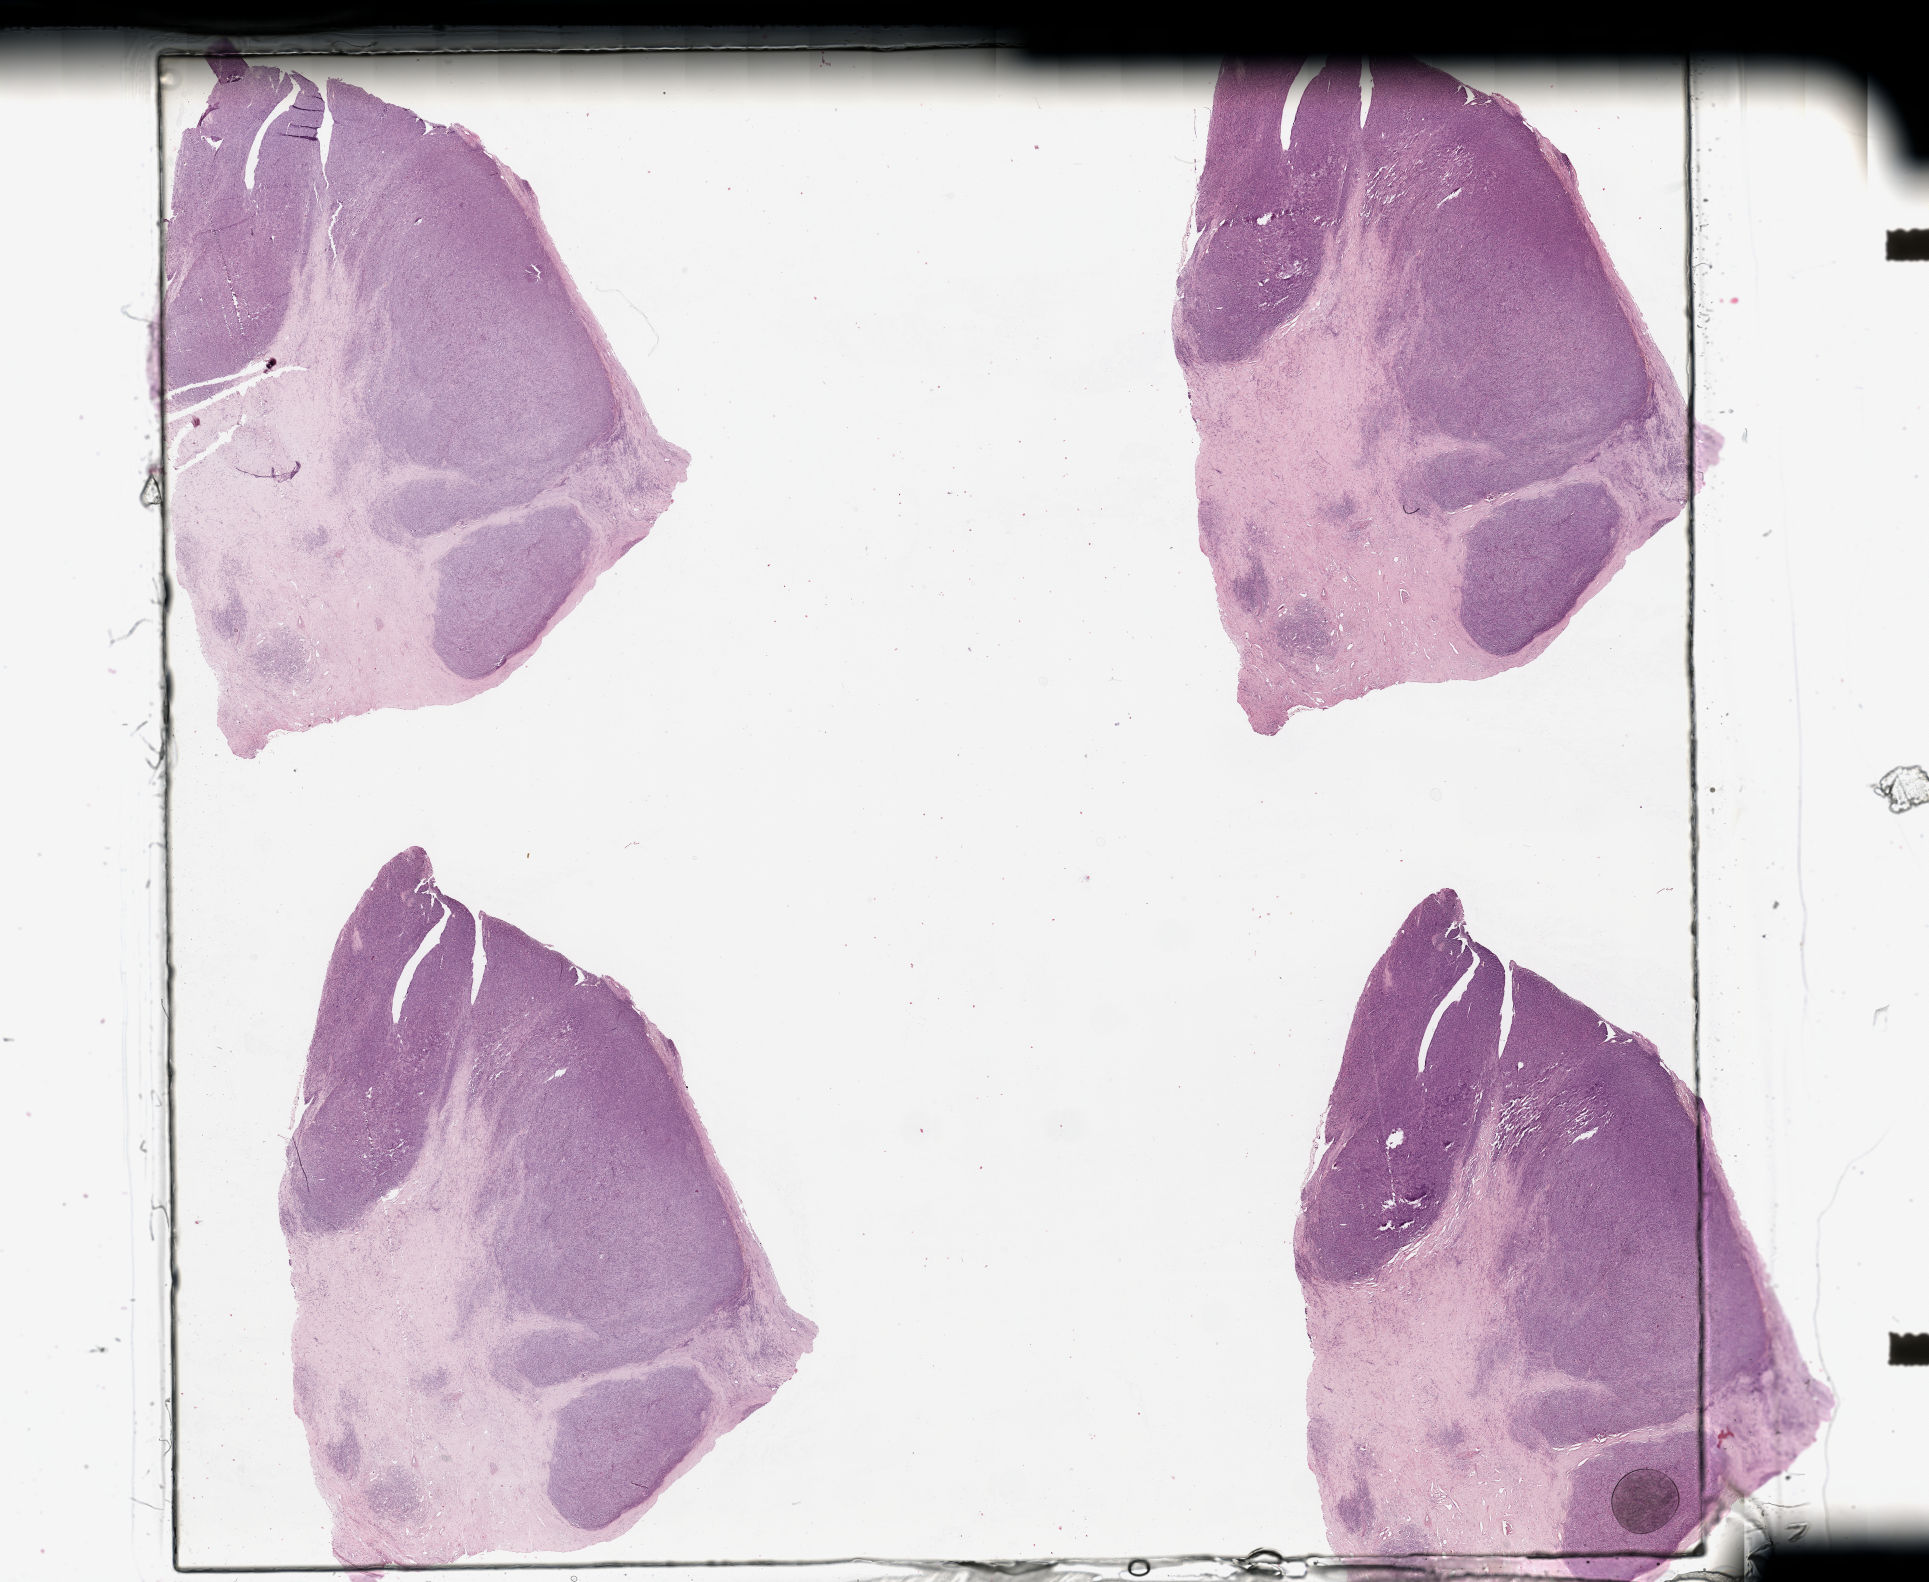
H&E whole-slide image, low-resolution overview of the scanned area, about 30.5 x 25.0 mm; tumour tissue sample. 52-year-old female patient.
Primary tumour site (as recorded): lower extremity. Patient diagnosis (cohort enrolment): sarcoma (site not recorded at cohort level).